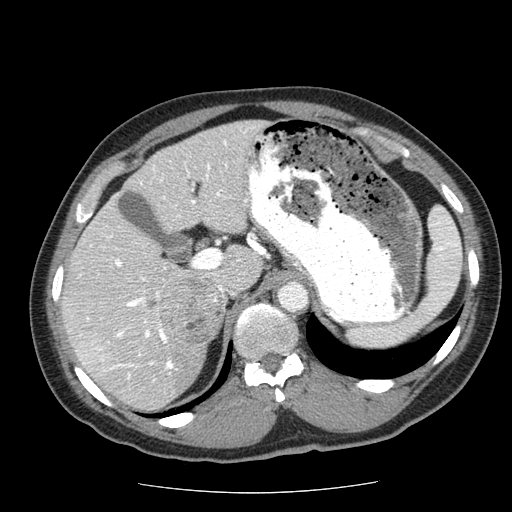
Contrast-enhanced abdominal CT (liver protocol), one axial slice; slice 37 of 85 in the series (ordered by position); soft-tissue window (W 400 / L 40 HU); 2.5 mm slice thickness; 512 × 512 image matrix, field of view 360 × 360 mm. Case-level facts recorded for this patient, not image findings: diagnosis: hepatocellular carcinoma (patient treated with transarterial chemoembolisation; whether this scan precedes or follows treatment is not stated here); TNM stage (as recorded): Stage-IIIA; Child-Pugh class: A; tumour nodularity: multinodular; tumour size: 8 cm.
Annotated regions visible in this slice (semi-automatic segmentation, software-assisted and operator-edited):
- abdominal aorta: bounding box <278,283,307,311> (left, top, right, bottom; pixels)
- liver parenchyma outside the tumour (the mass and vessels are separate outlines, so this box may not span the whole liver): <62,120,267,410>
- mass: <145,275,222,344>
- liver vessels: <80,127,254,379>